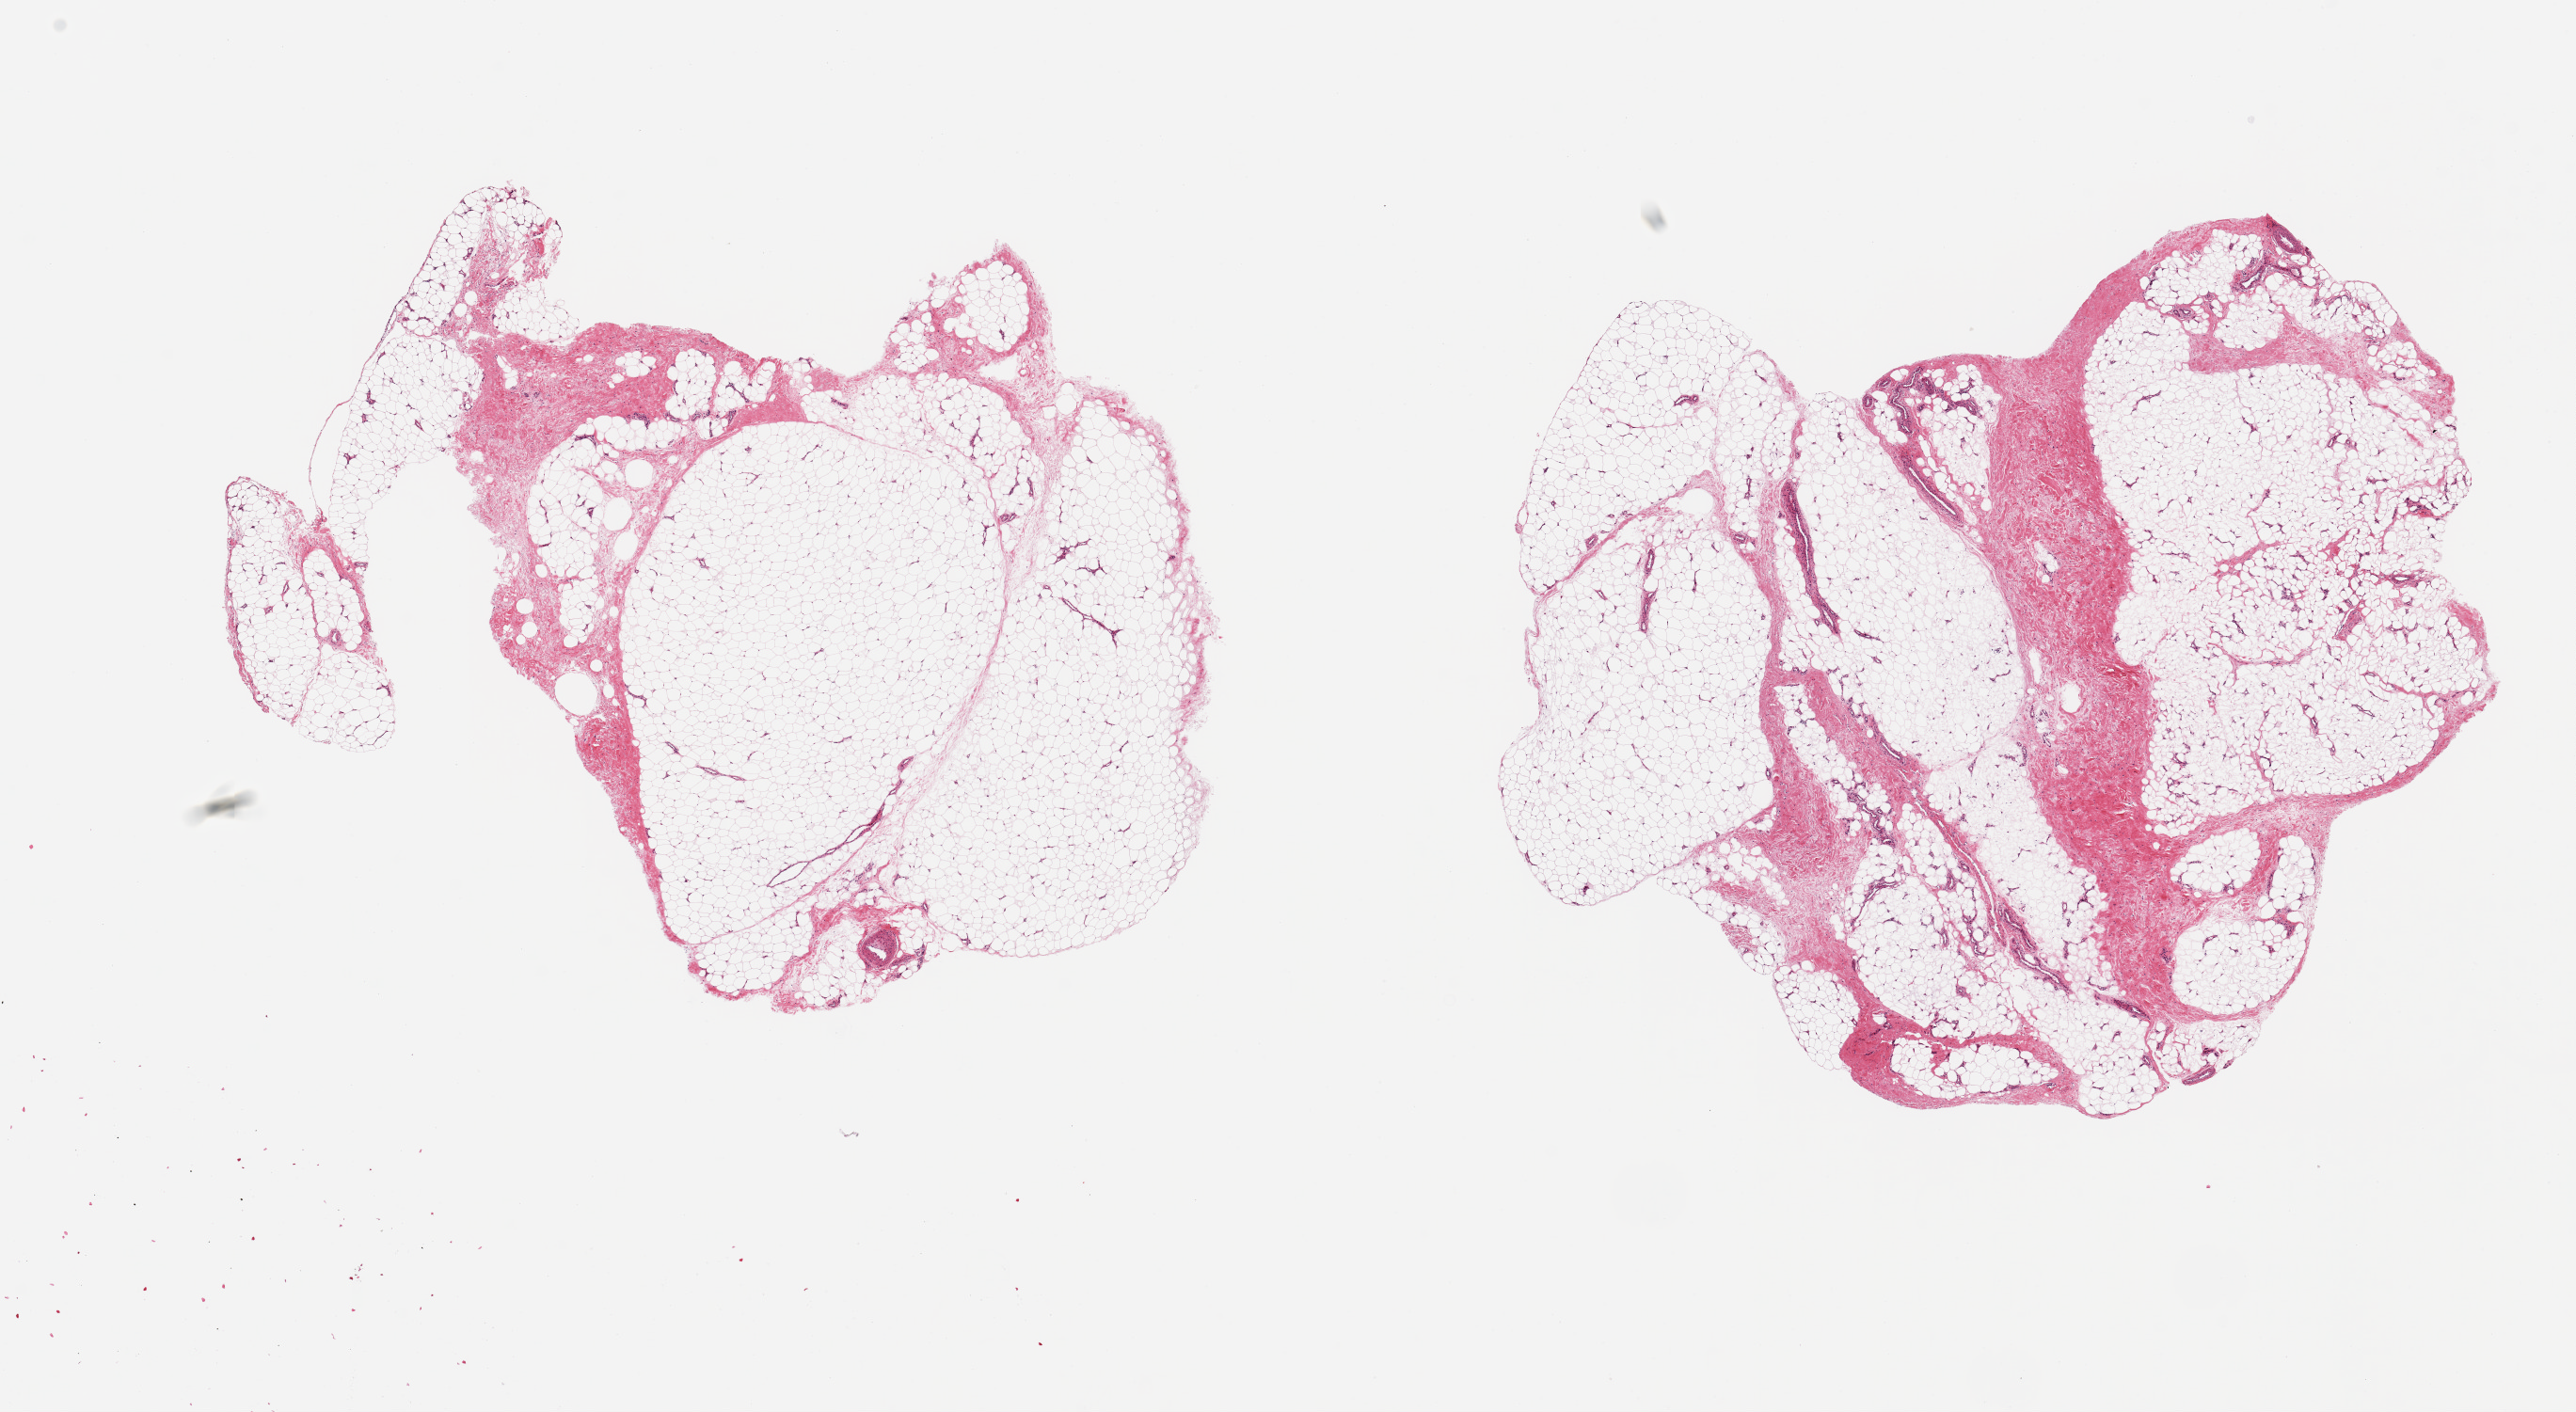
Digitized haematoxylin and eosin-stained section, brightfield — low-resolution overview of the scanned area, about 21.7 x 11.9 mm (slide scanned at 20x). PAXgene-fixed, paraffin-embedded tissue. Target tissue: adipose tissue. Donor tissue sample. Donor: male.
- pathologist's review note for this sample: 2 pieces 9x7 & 8.5x7mm